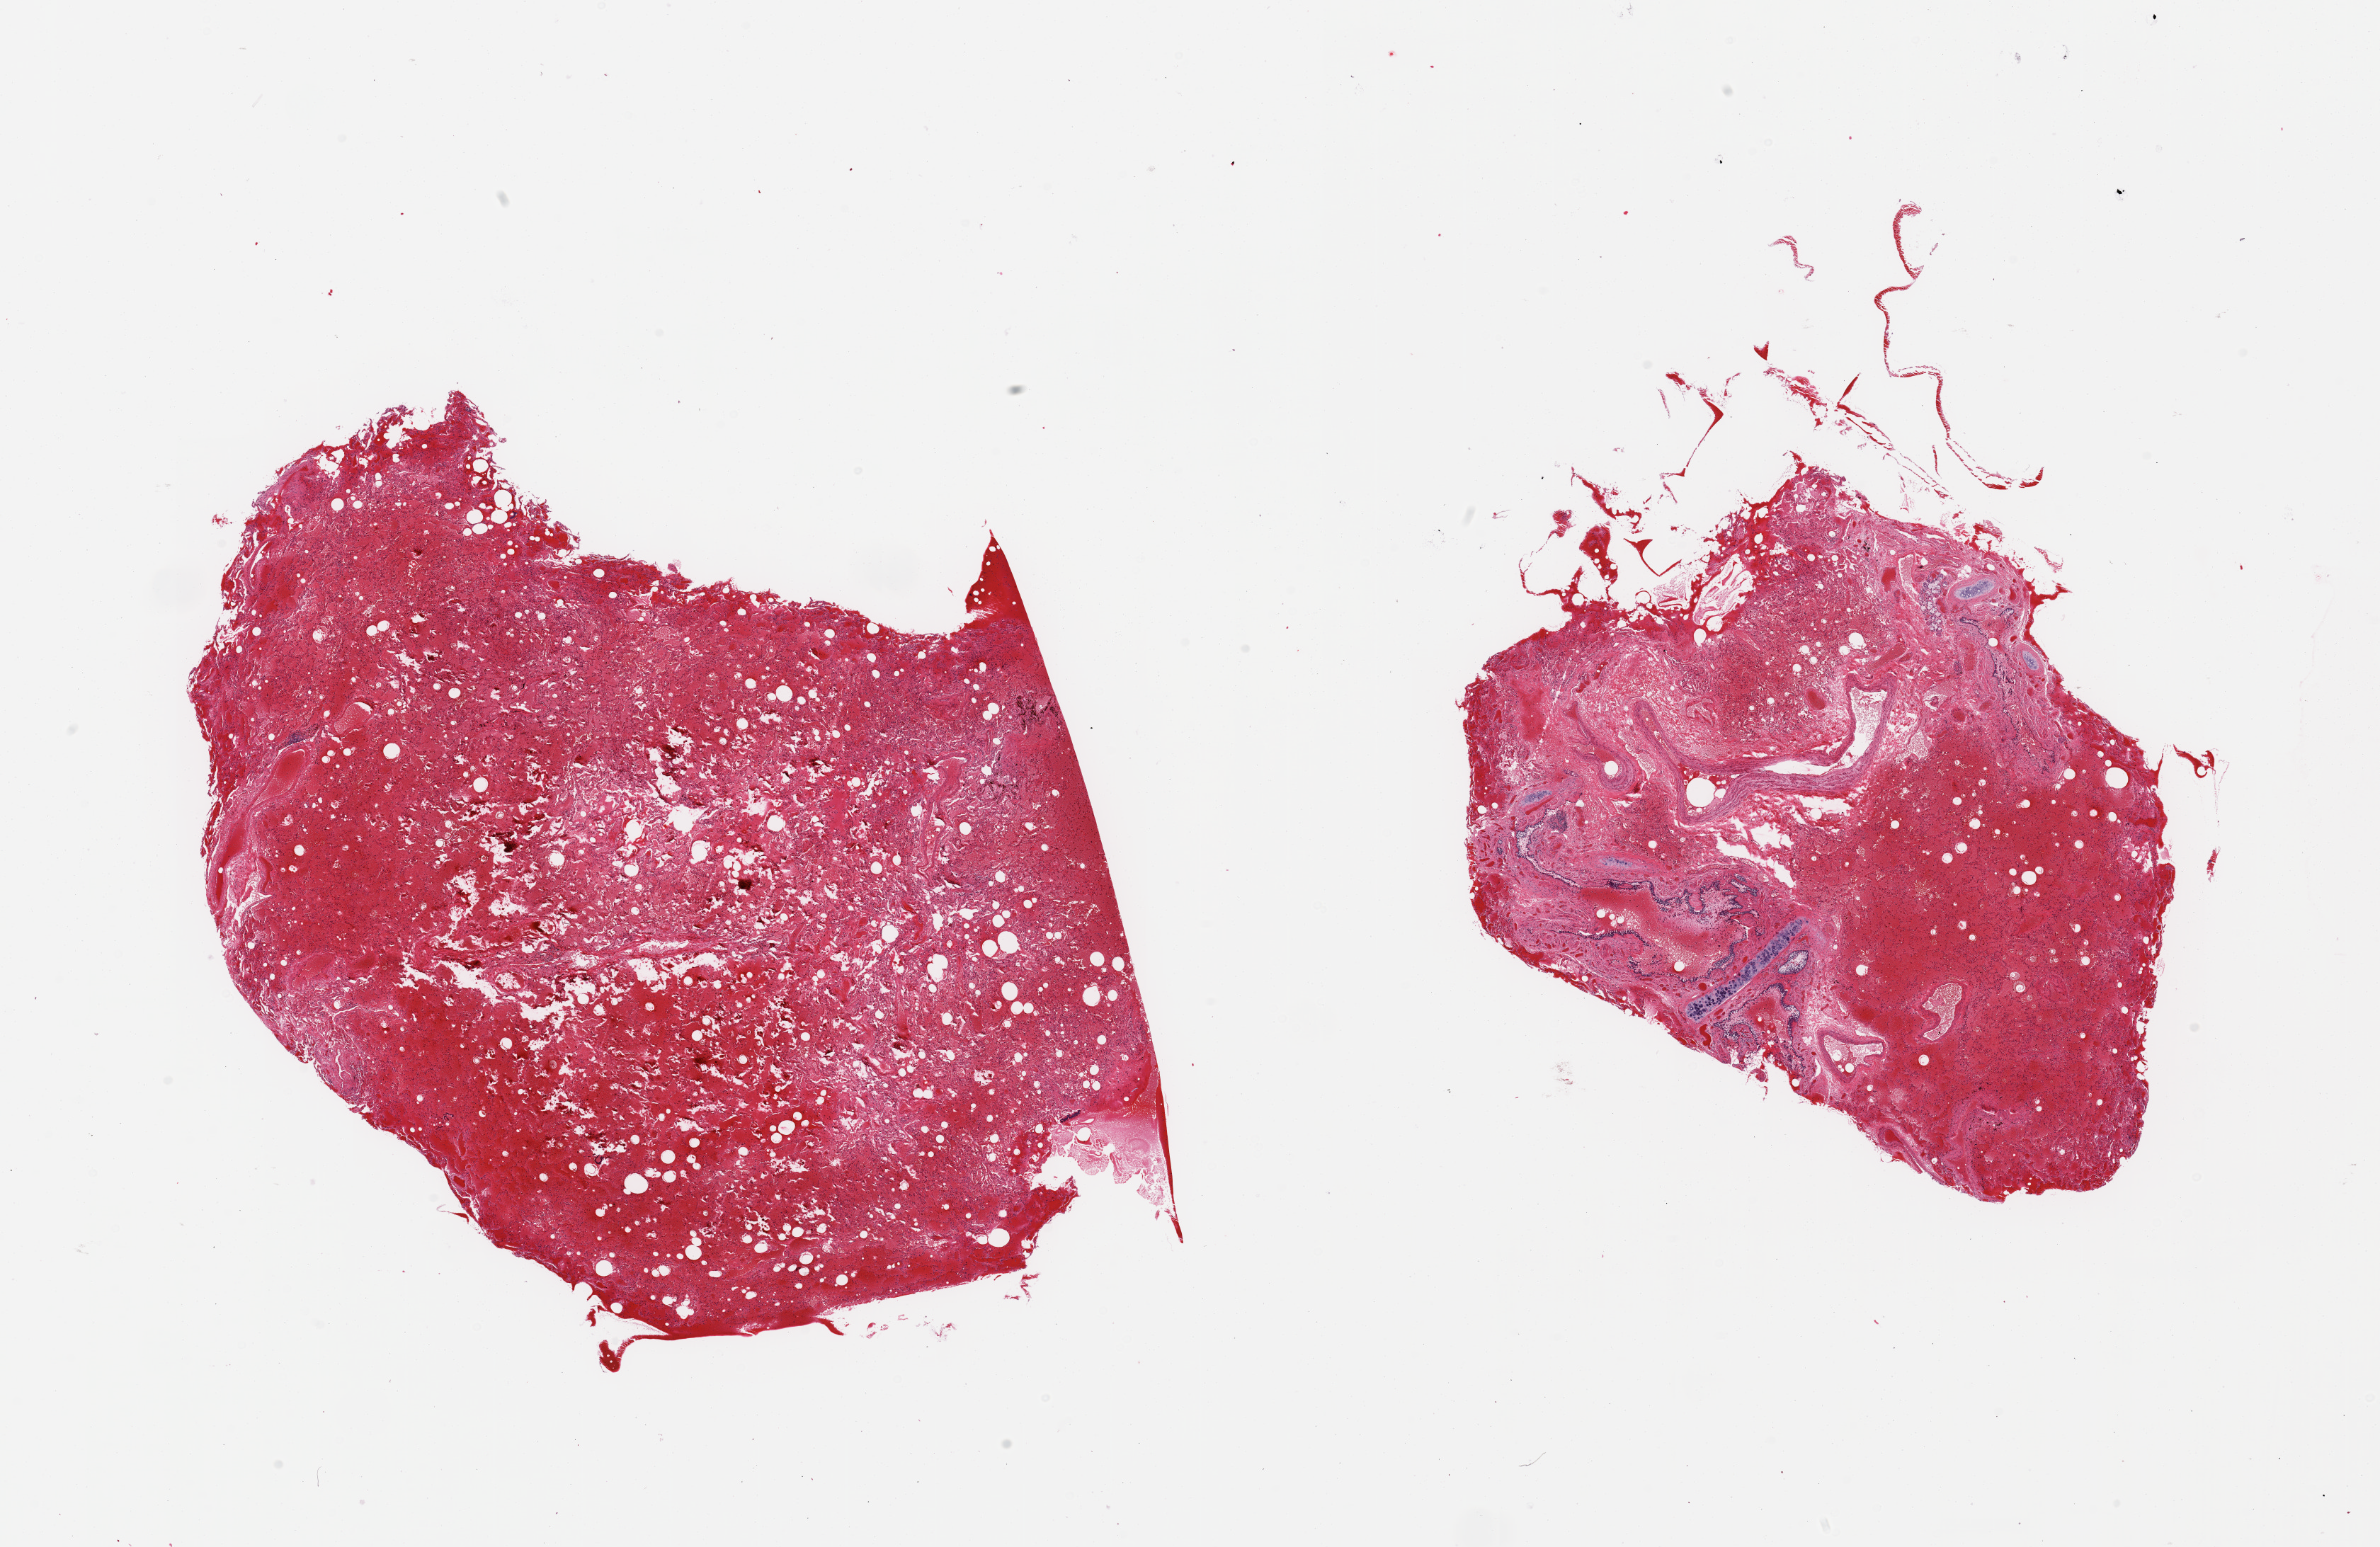
Whole-slide image, haematoxylin and eosin stain, whole scanned area (about 26.6 x 17.3 mm) shown as a low-resolution overview. PAXgene-fixed, paraffin-embedded tissue. Section of lung (target tissue). Donor tissue sample.
Reviewer comment on this tissue sample: 2 pieces, marked congestion; Hyaline cartilage foci present.